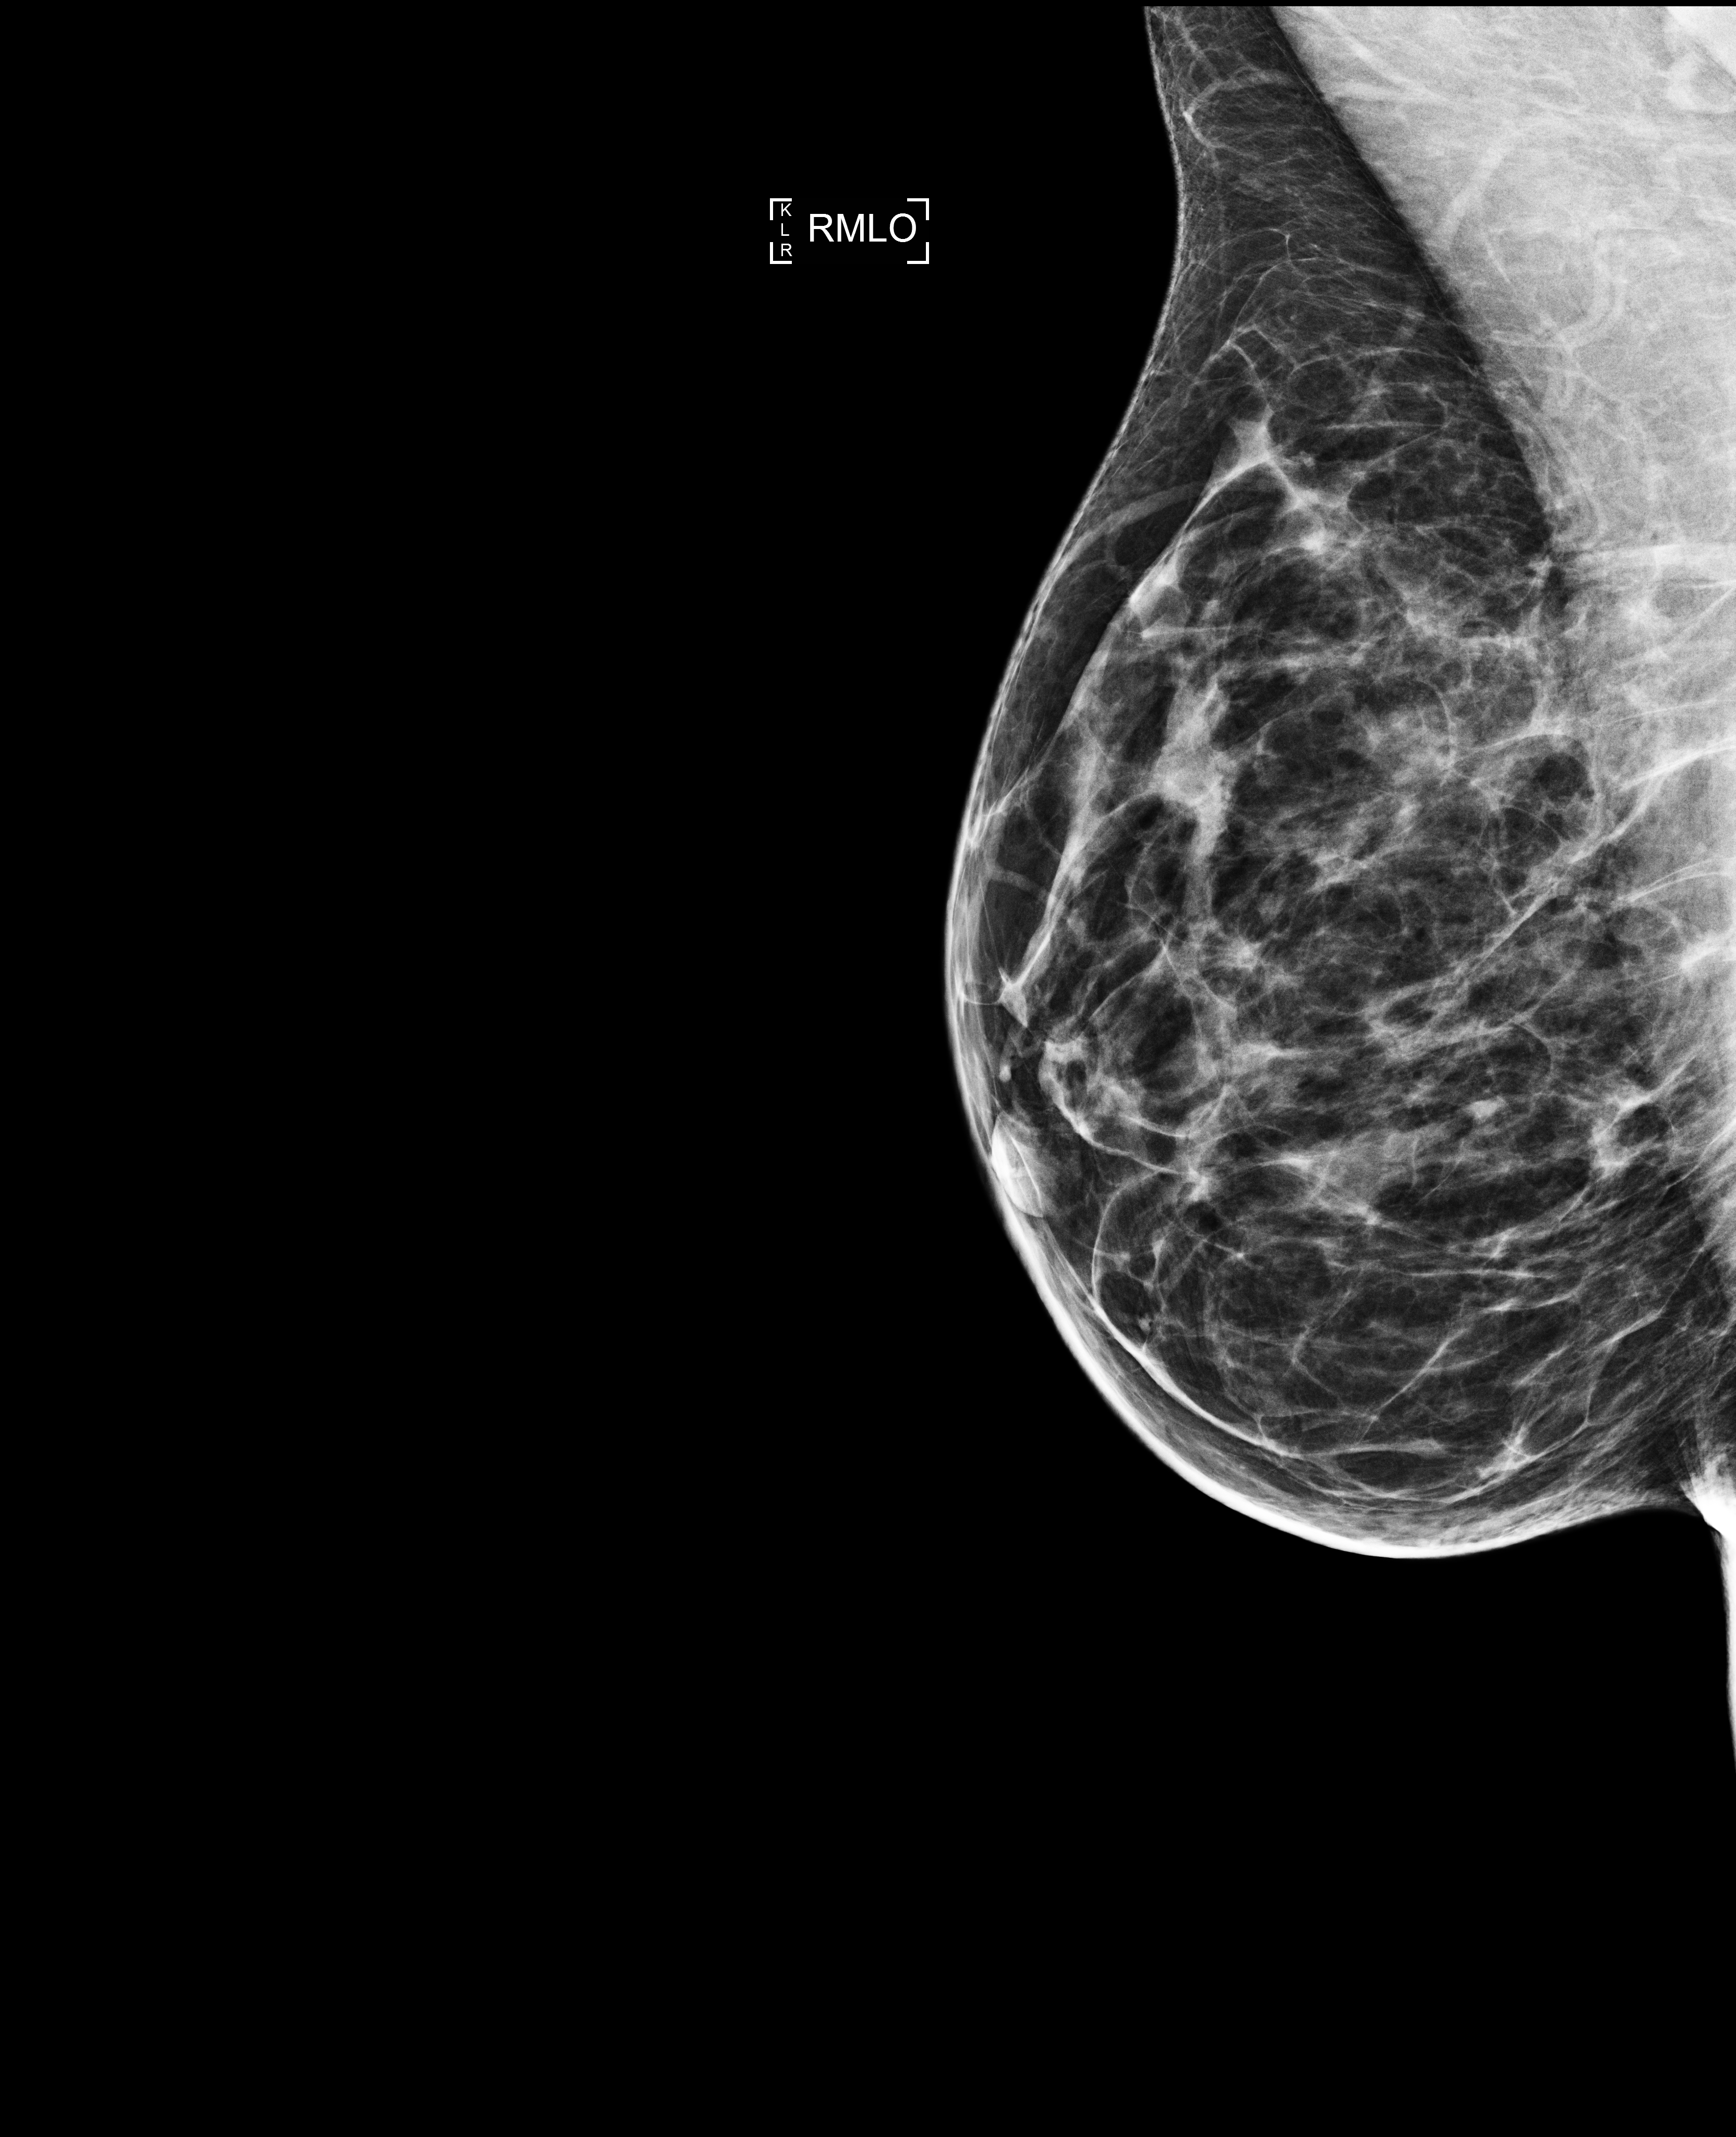
Annual screening mammography examination. Patient: female, 41 years.
Image type: full-field digital mammogram. Breast: right. Projection: MLO view.